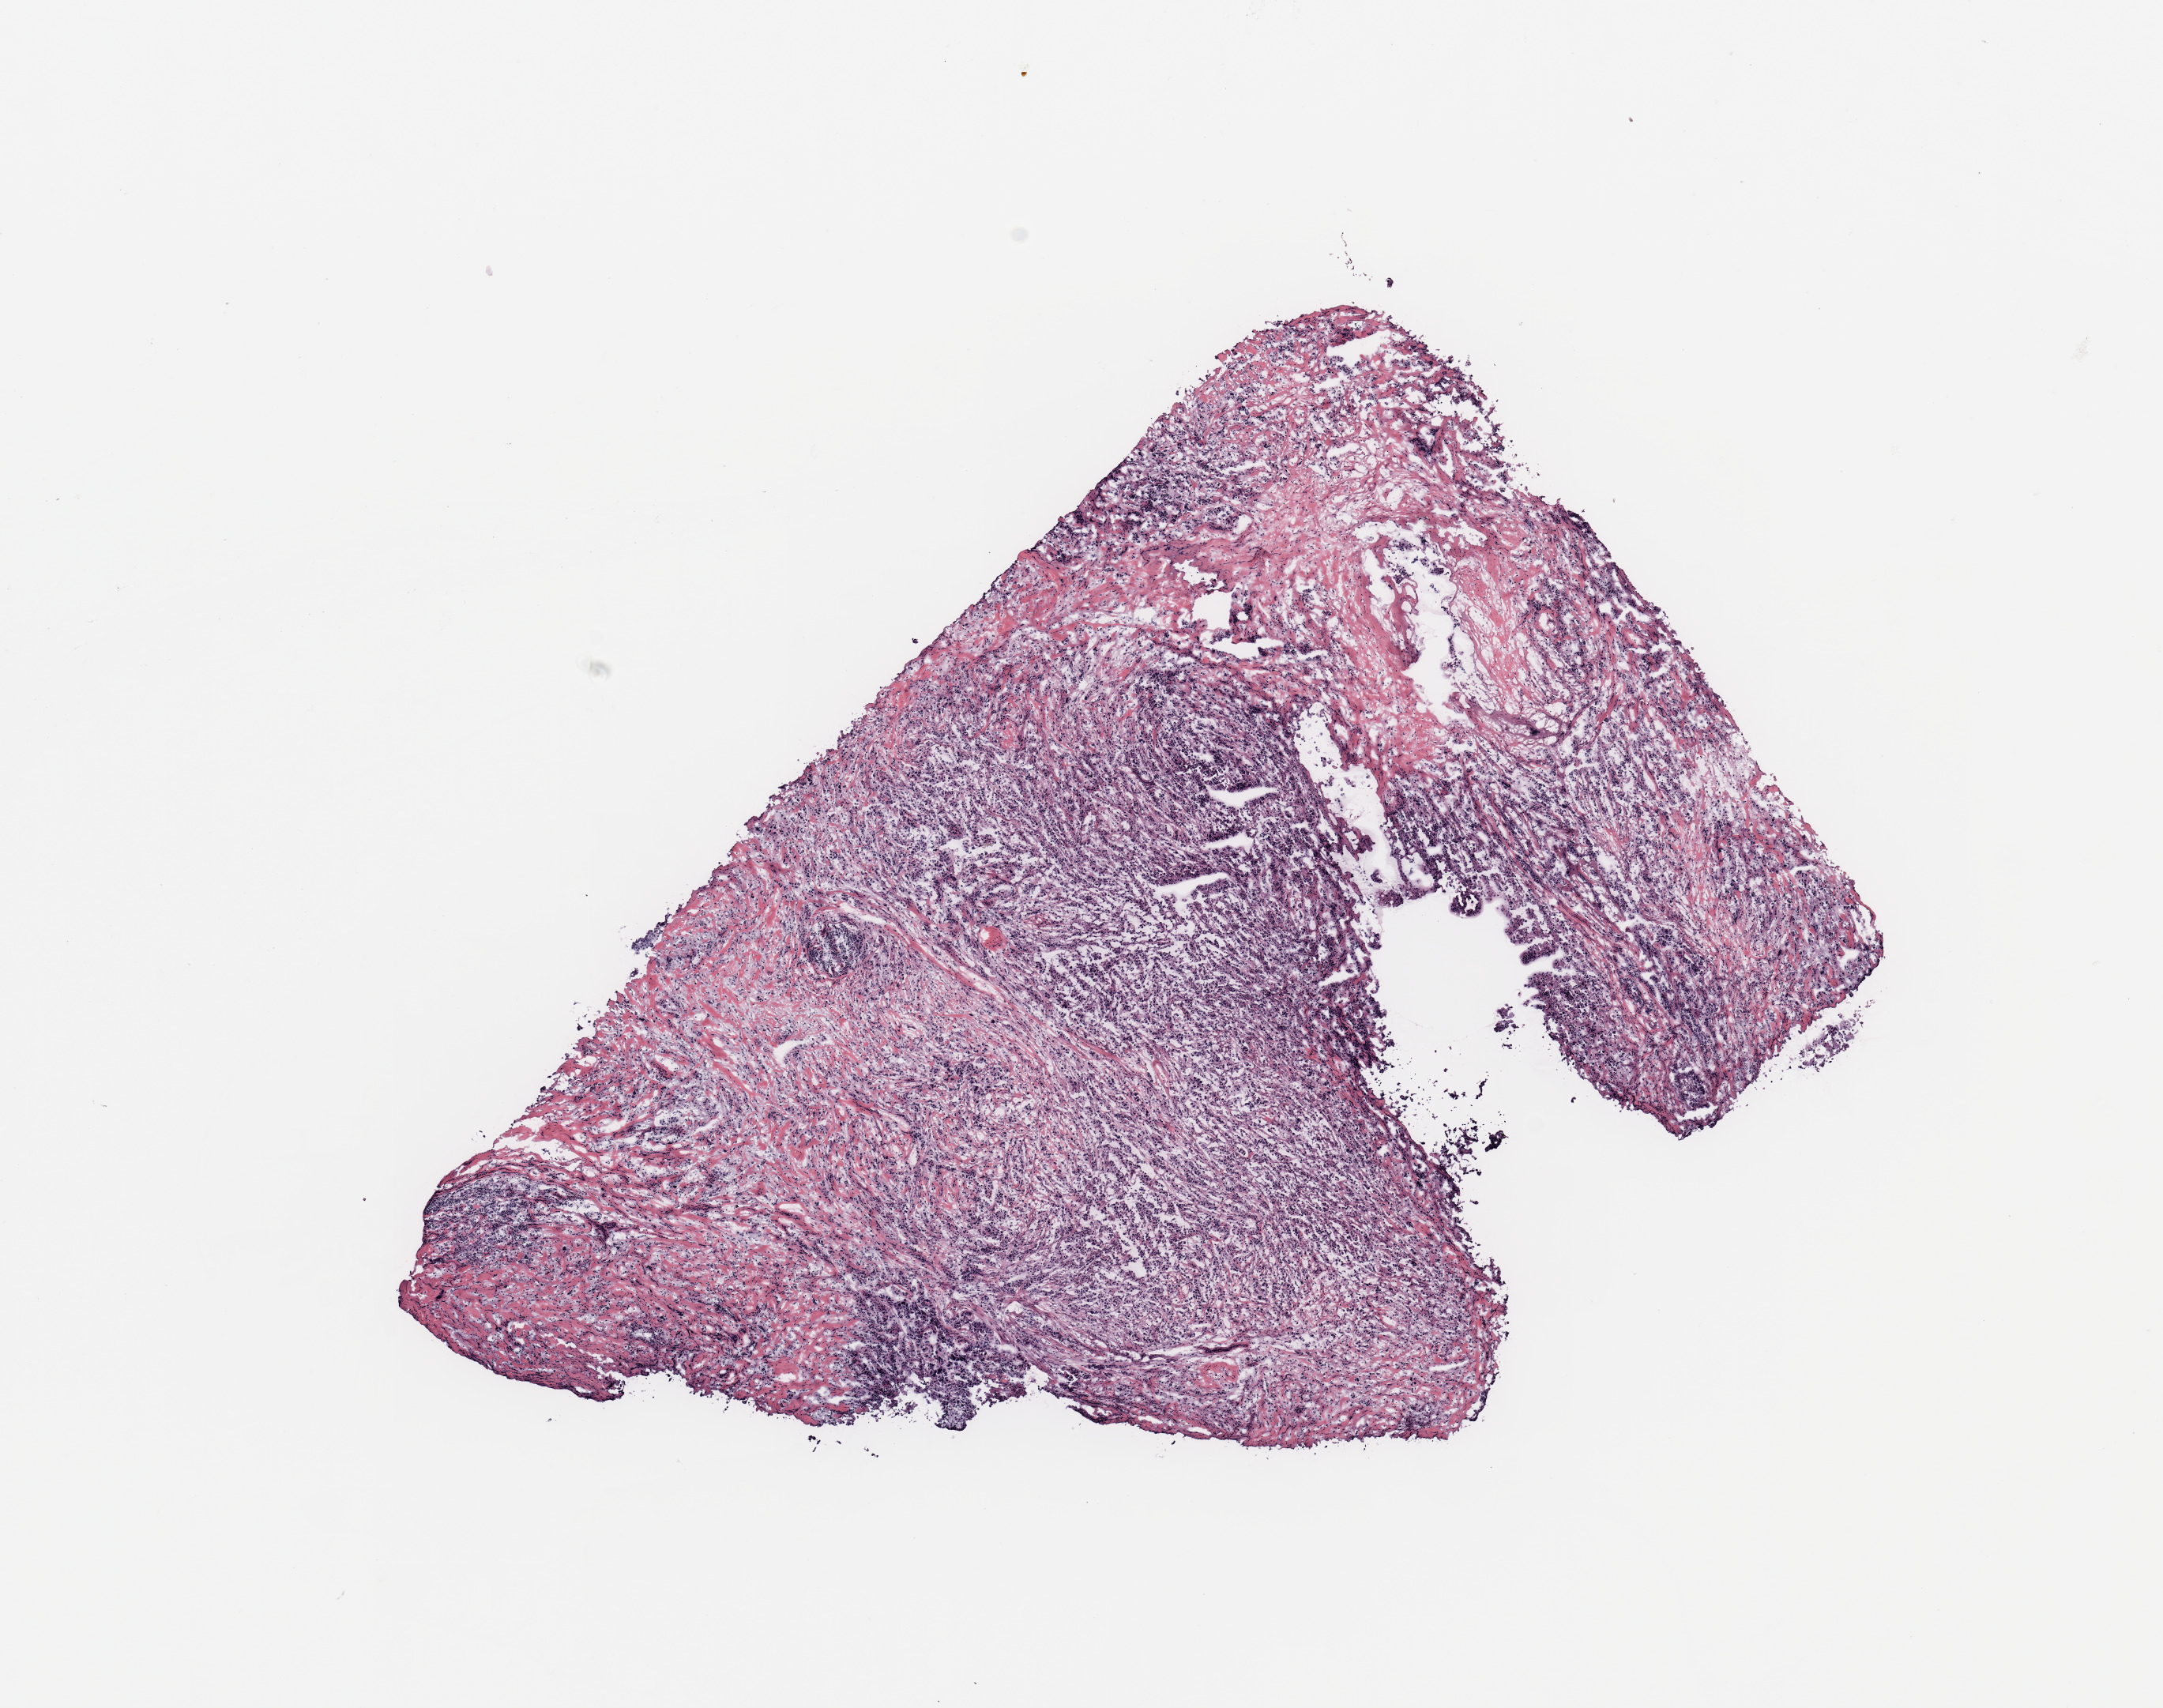
Whole-slide histology image, H&E-stained — shown as a low-resolution overview of the whole scanned area (about 10.8 x 8.6 mm, slide scanned at 20x). Tumour tissue sample, breast. Patient: female, age 50 years.
* histologic diagnosis: Infiltrating duct carcinoma, NOS
* AJCC pathologic stage: IIB